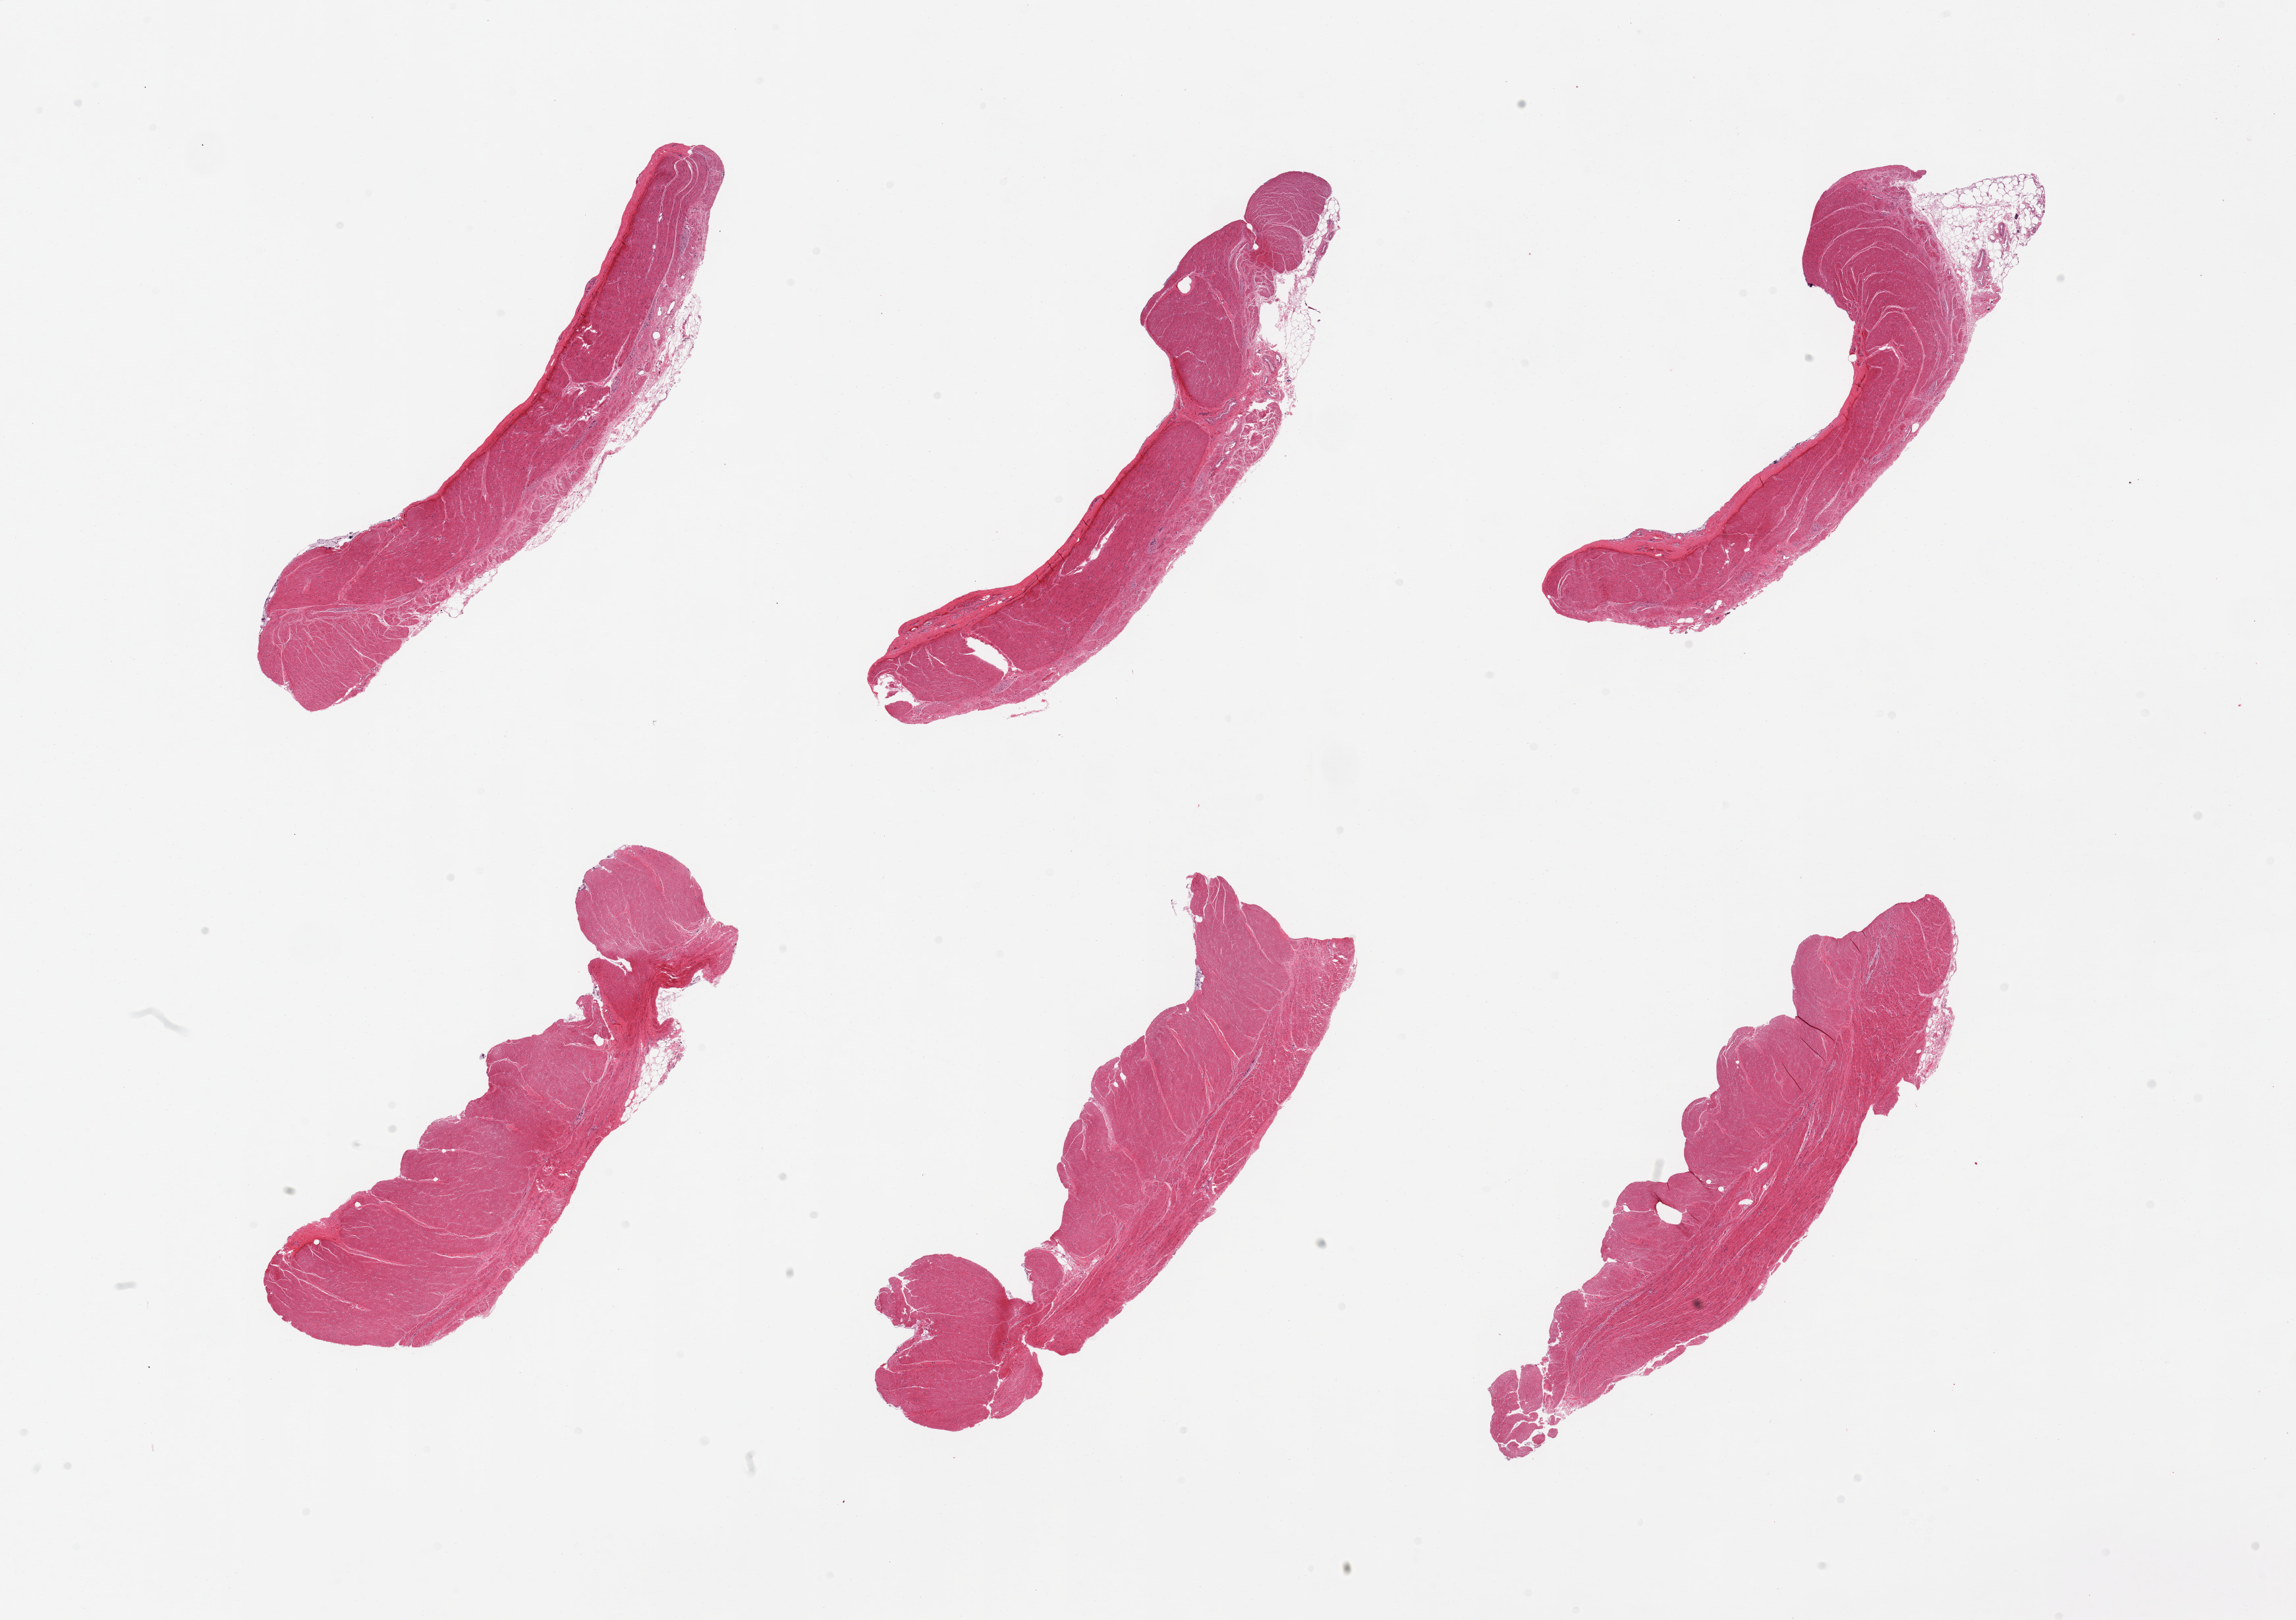
Digitized H&E-stained section — shown as a low-resolution overview of the whole scanned area (about 27.6 x 19.4 mm, from a 20x scan), PAXgene-fixed, paraffin-embedded tissue, target tissue: sigmoid colon, donor tissue sample. Donor sex: male.
Reviewer comment on this tissue sample: 6 pieces; predominantly well trimmed.